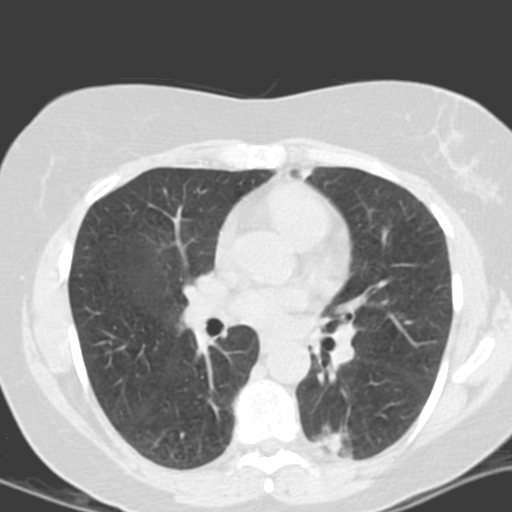
Low-dose screening chest CT, axial slice; second annual screen; lung window (W 1500 / L -600 HU); 3.2 mm slice thickness; 120 kVp; slice 69 of 161 in the series. Female participant, aged 55 years at enrolment. Current smoker at enrolment.
Expert reader's lesion annotation, bounding box (x1, y1, x2, y2) in pixels: (304, 410, 379, 470). The screening reader recorded 4 non-calcified nodules or masses ≥4 mm on this exam (left lower lobe, left lower lobe, left upper lobe, right middle lobe); which of them this box marks is not recorded. Lung cancer was diagnosed 688 days after this screen: adenocarcinoma with mixed subtypes, left lower lobe, poorly differentiated (G3), stage IA (AJCC 6th edition), 21 mm at pathology.